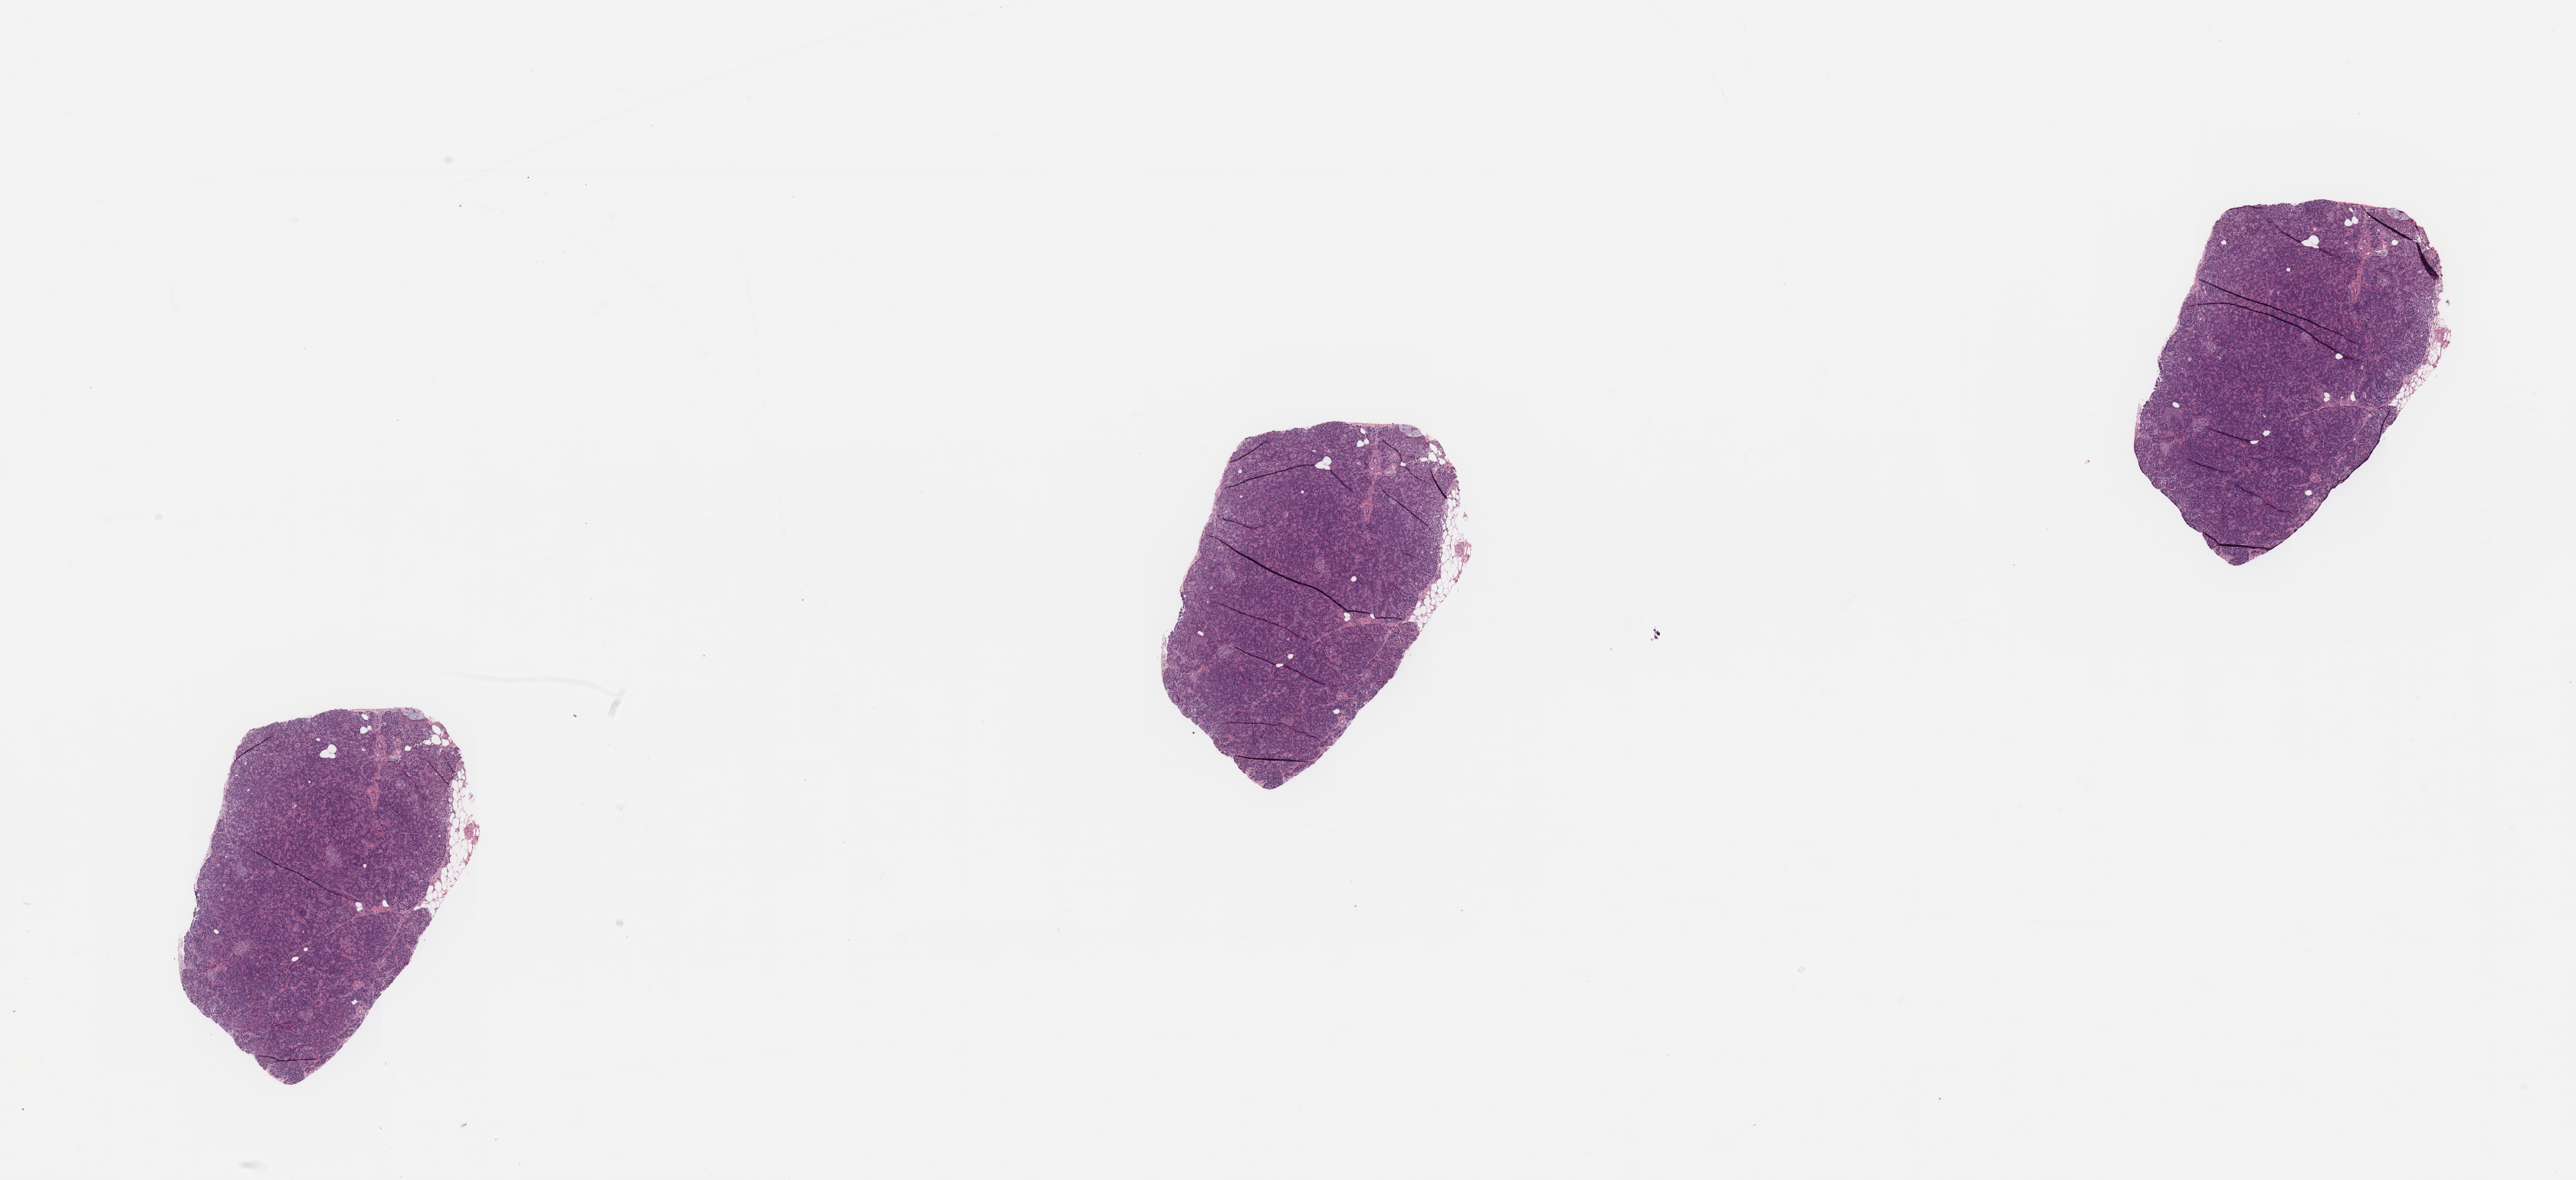
Digitized H&E-stained tissue section (whole slide), shown as a low-resolution overview of the whole scanned area (about 26.6 x 12.2 mm, slide scanned at 20x); pancreas, normal (non-tumour) tissue. Male, 76 y/o.
This section: normal (non-tumour) tissue from the same patient. Patient diagnosis: Infiltrating duct carcinoma, NOS.